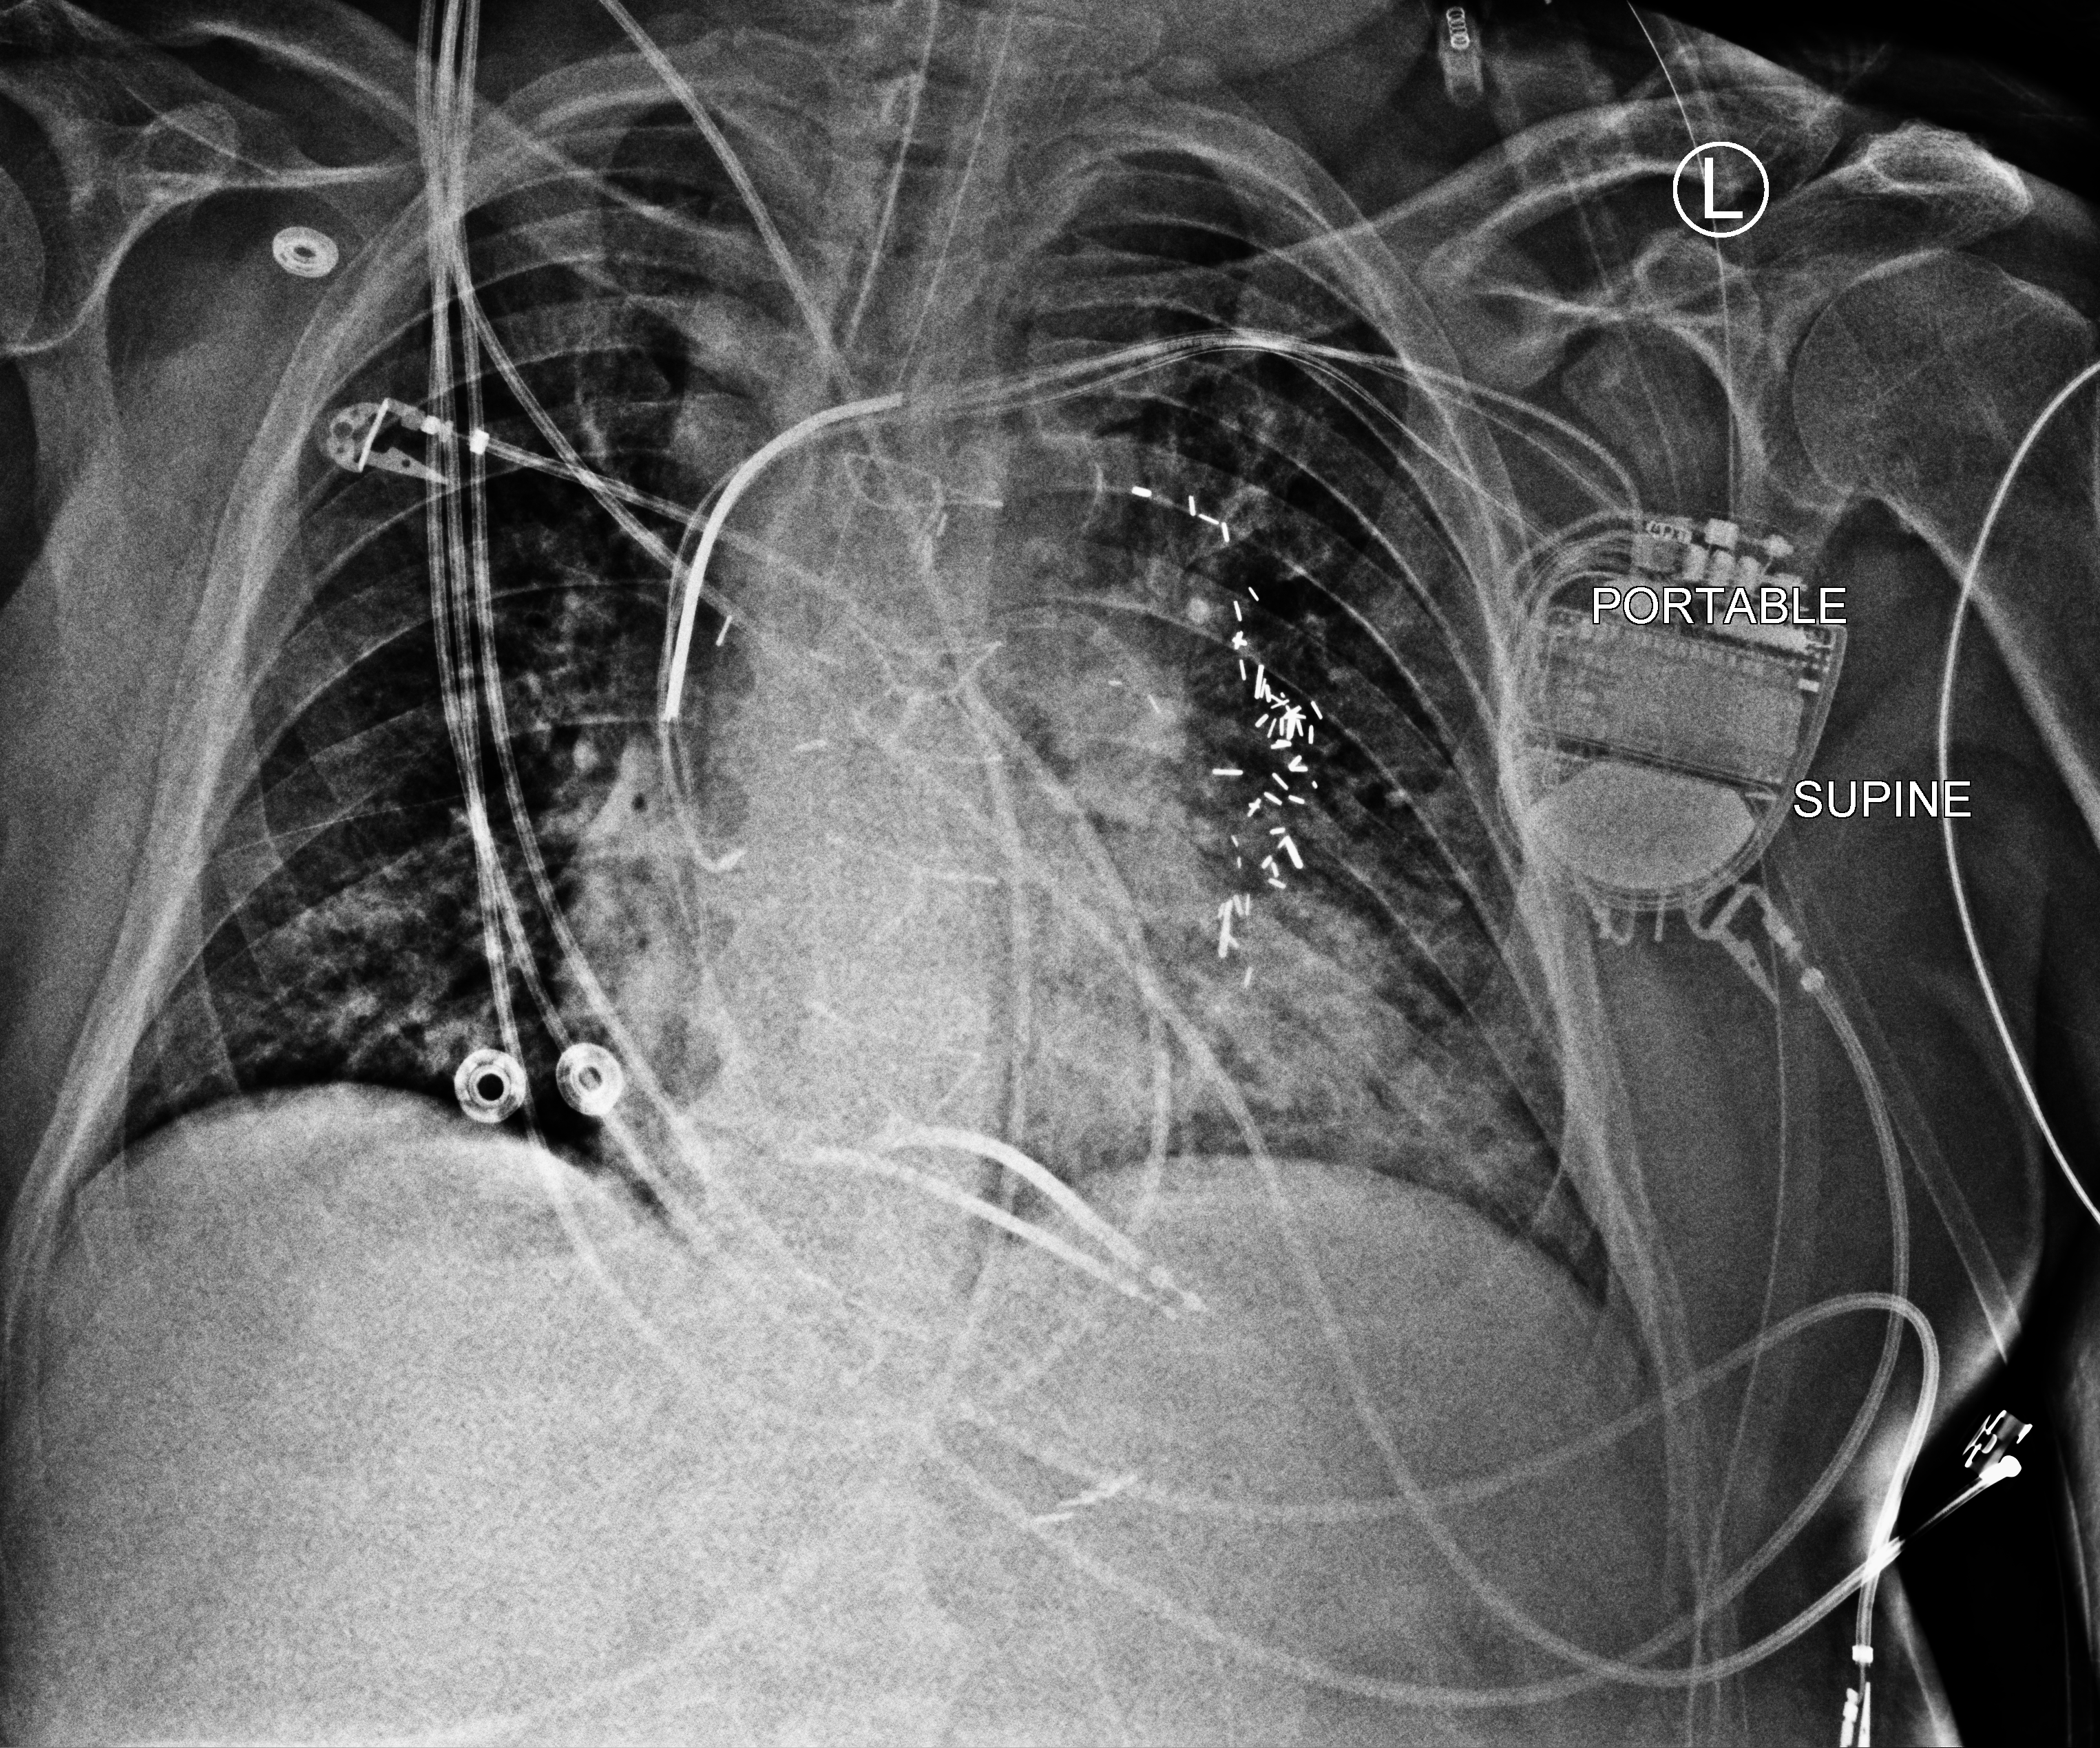
Bedside chest radiograph (computed radiography), anteroposterior (AP) projection. Patient hospitalised with COVID-19; male, aged 60–74 years.
Hospital-stay facts (about this admission, not read from this image; timing relative to this image not recorded): mechanically ventilated during this hospital stay: yes; admitted to intensive care during this hospital stay: yes; chronic kidney disease (admission record): no.